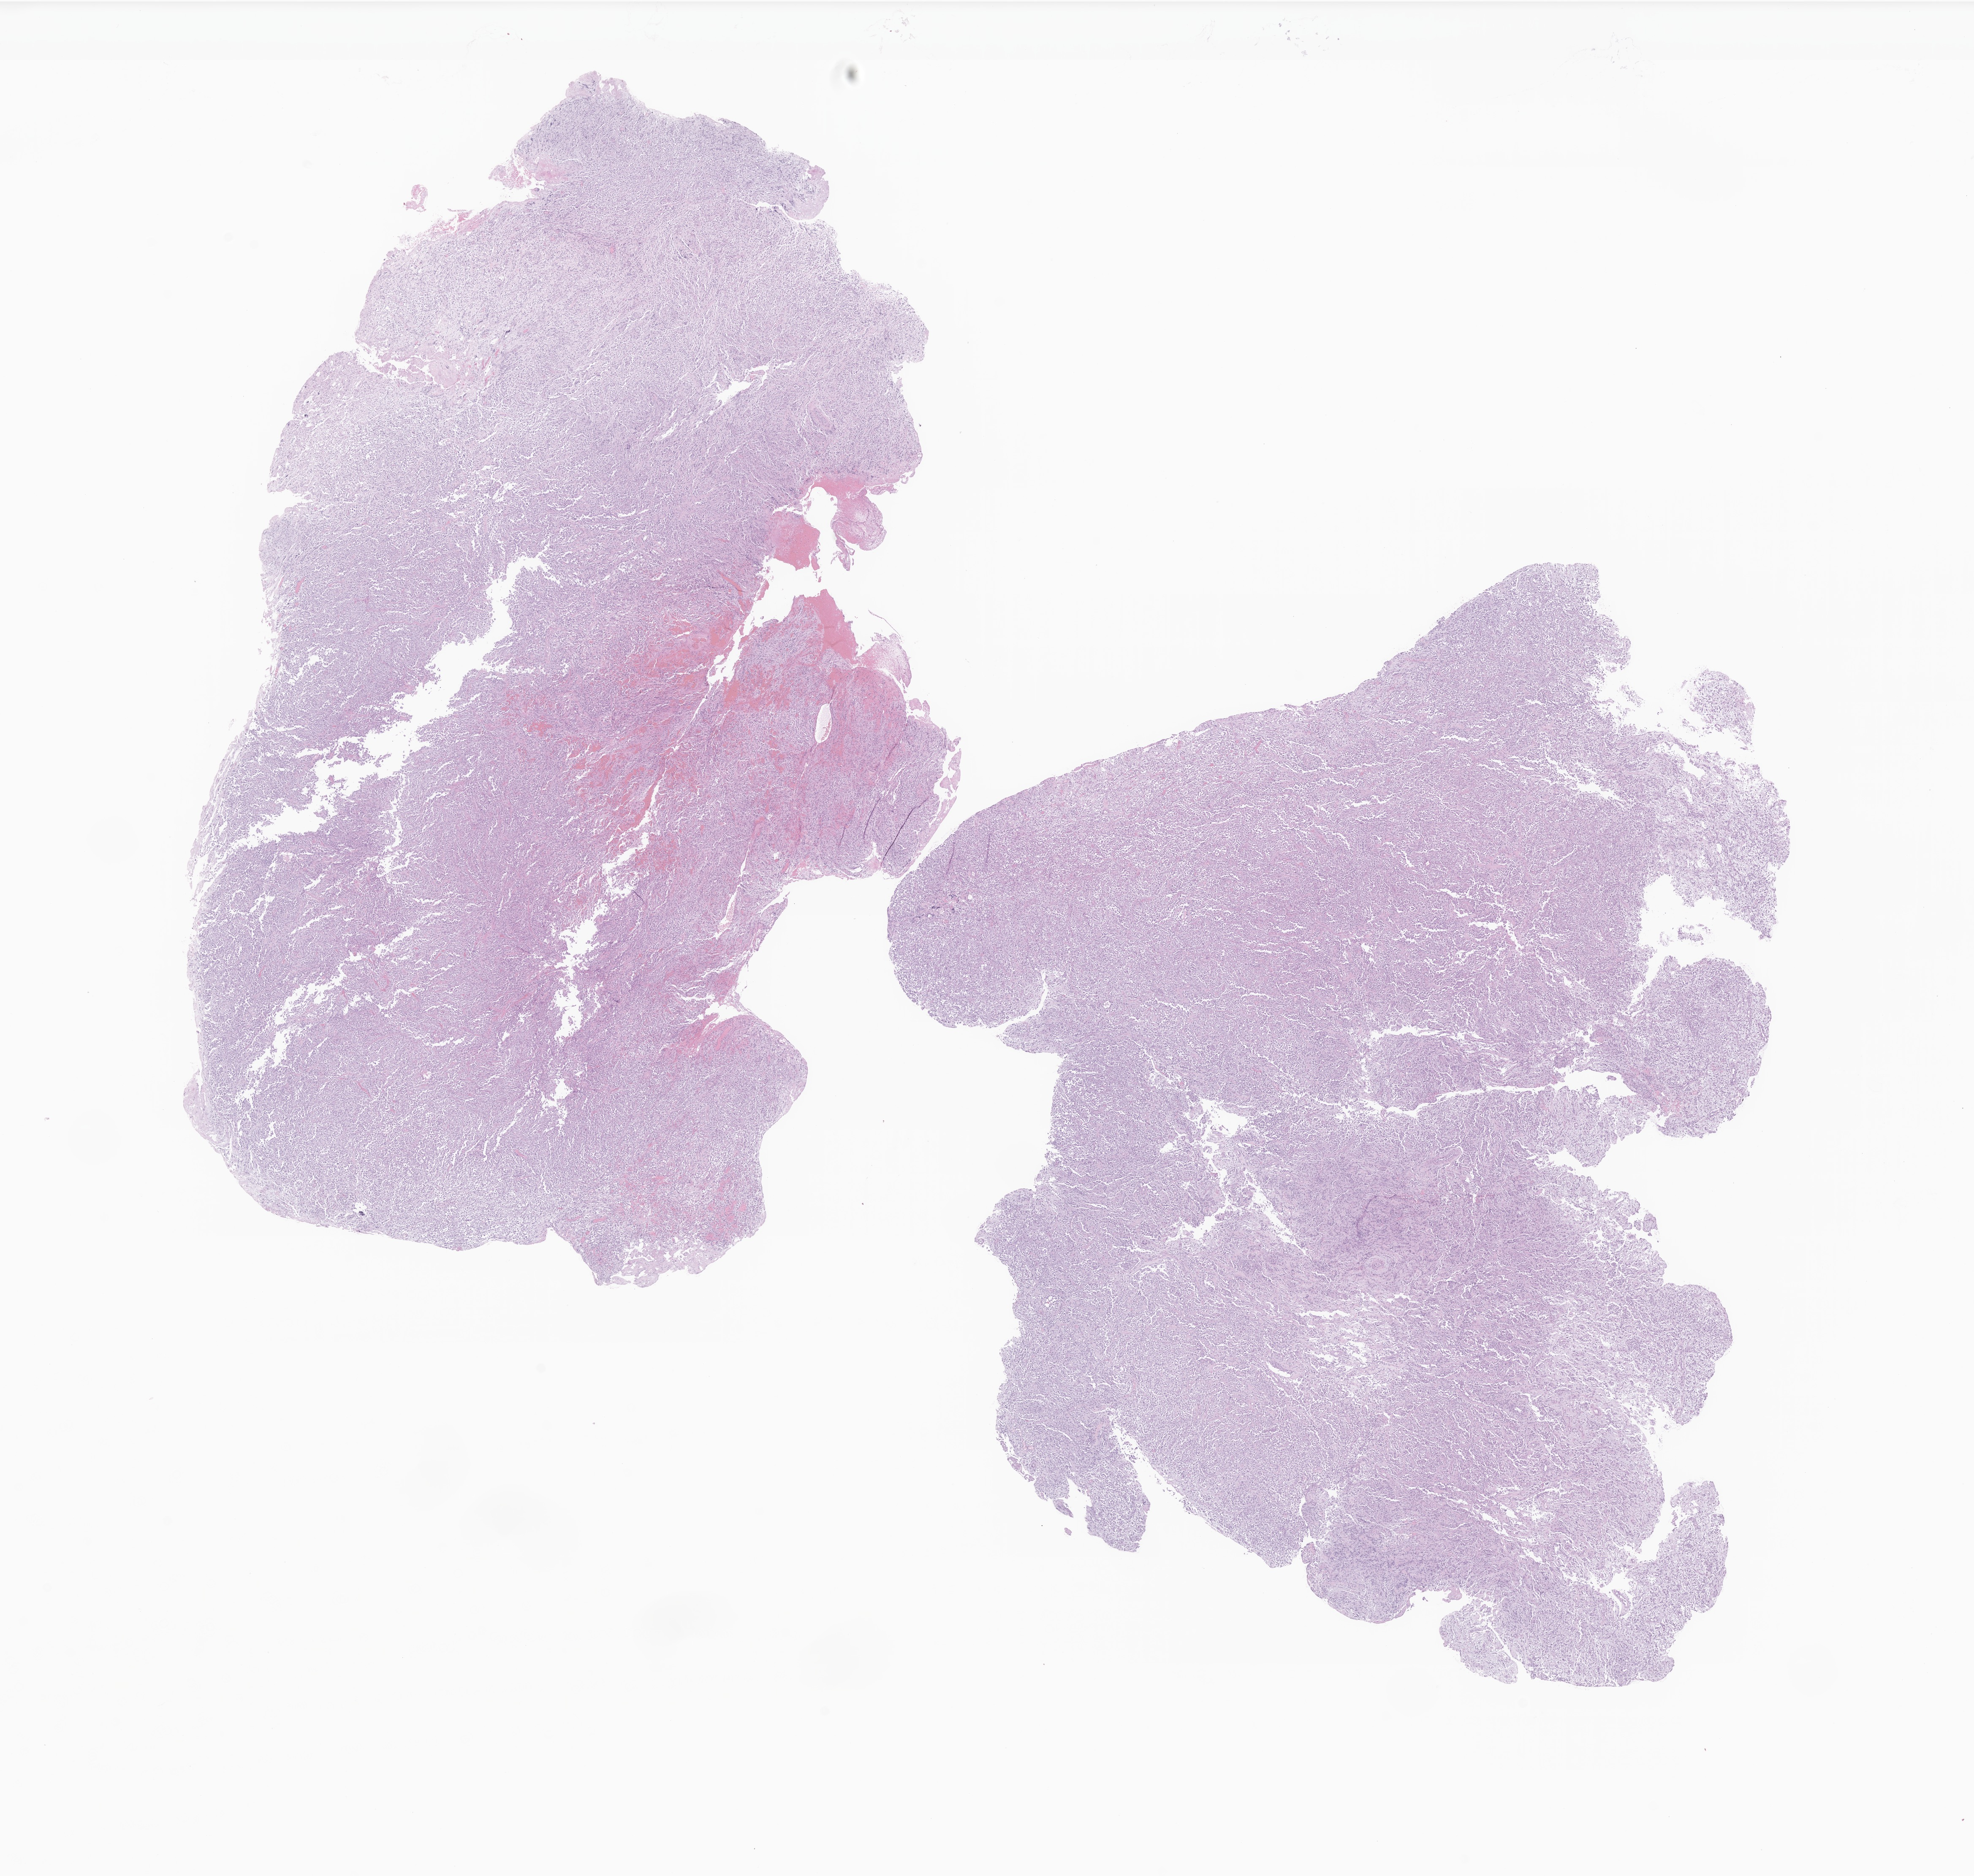
Digitized H&E-stained section of tumor tissue from the brain, a low-resolution overview of the entire scanned area, about 19.7 x 18.7 mm; formalin-fixed, paraffin-embedded (FFPE) tissue. Patient: male, age 320 days.
* diagnosis (ICD-O-3 morphology term): Histiocytic sarcoma